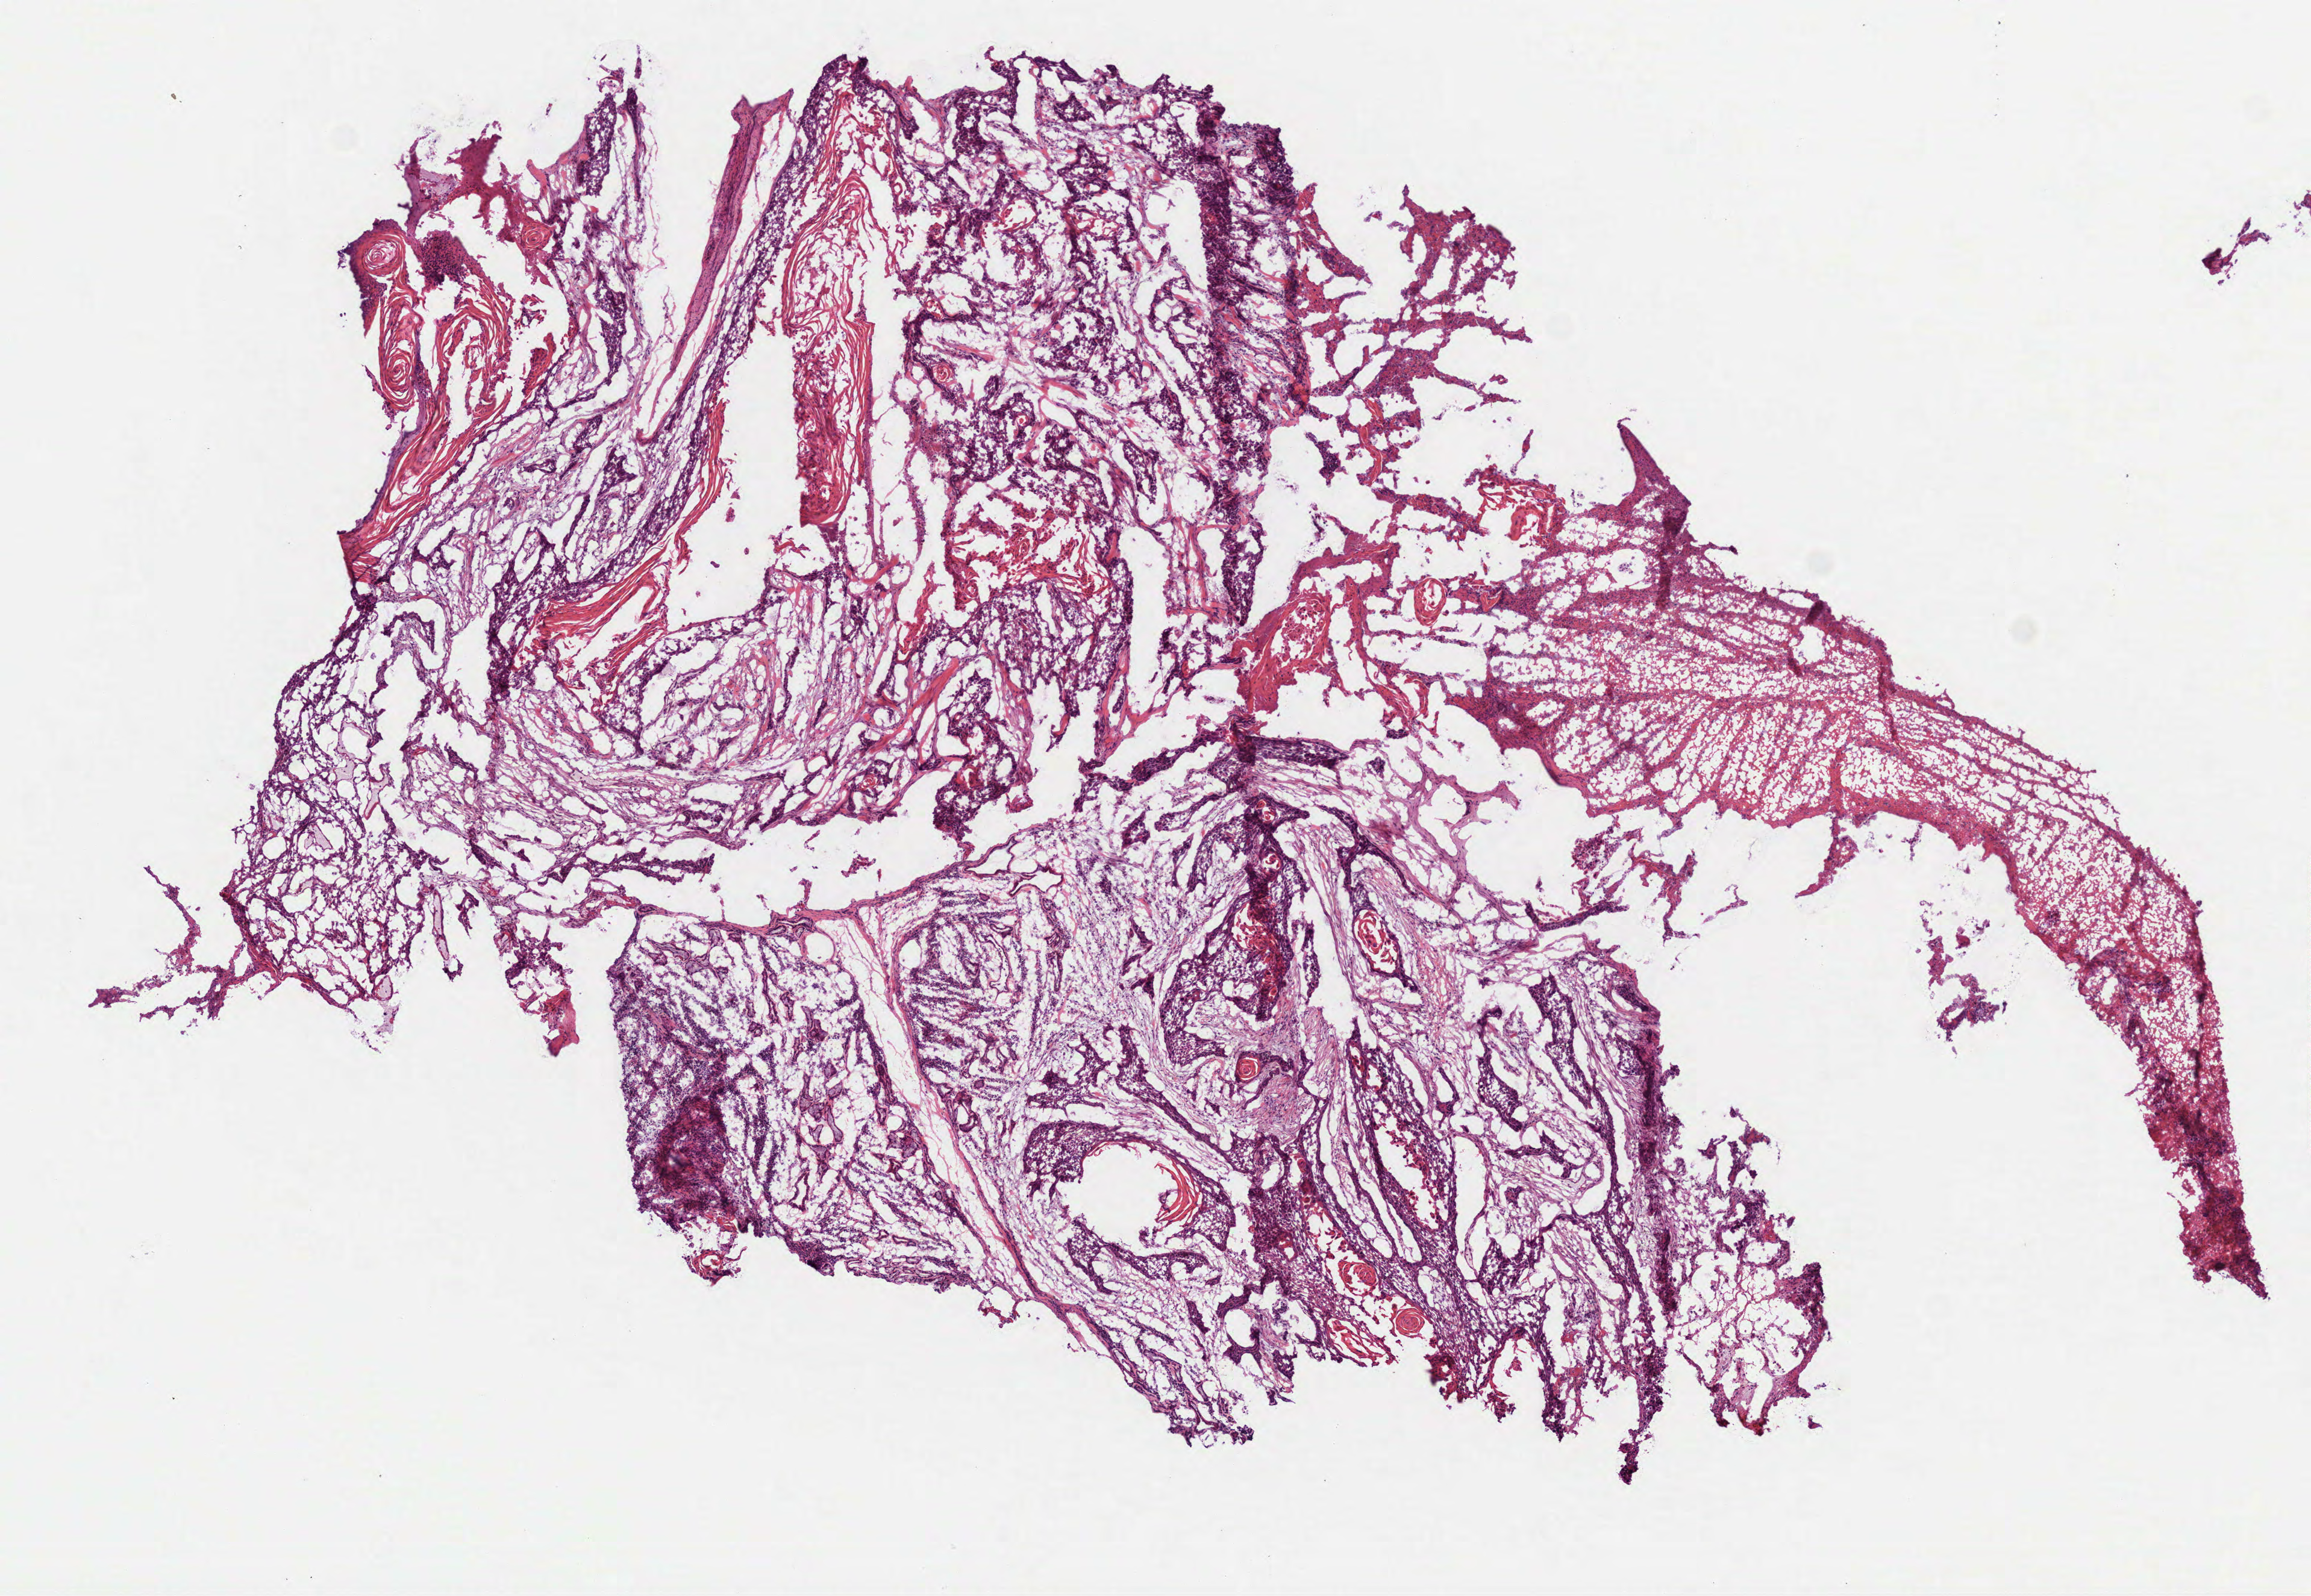
Digitized H&E-stained tissue section (whole slide), shown as a low-resolution overview of the whole scanned area (about 7.7 x 5.3 mm, acquisition: 40x scan). Frozen section from the top of the tissue portion. Head and neck, primary tumour sample. Patient: male, age at initial diagnosis 57 years. Histologic grade: G2 (moderately differentiated). Slide review estimates, as recorded: tumour cells 80%, tumour nuclei 80%, normal cells 0%, stromal cells 20%, necrosis 0%.
Pathologic diagnosis: Squamous cell carcinoma, NOS (larynx, NOS). AJCC pathologic stage: IVA (7th edition).